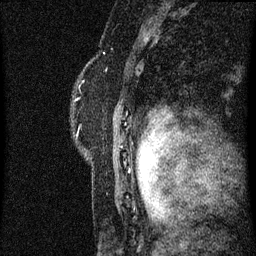
Breast MRI (dynamic contrast-enhanced), one sagittal slice; position 49 of 60 along the scan axis; dynamic contrast-enhanced series, image 2 of 3 at this slice position (ordered by acquisition); 1.5 T; TE 4.2 ms, TR 8 ms; 2 mm slice thickness; 256 × 256 image matrix, field of view 180 × 180 mm. Patient: female, 47 years.
Annotated regions visible in this slice (semi-automatically segmented with operator editing):
- analysis volume of interest (the breast-tissue region the enhancement analysis was run in; not a lesion): bounding box <73,82,147,187> (left, top, right, bottom; pixels)
- tumour enhancement mask (voxels above the 70 % enhancement threshold inside the analysis volume of interest): <143,156,147,163>